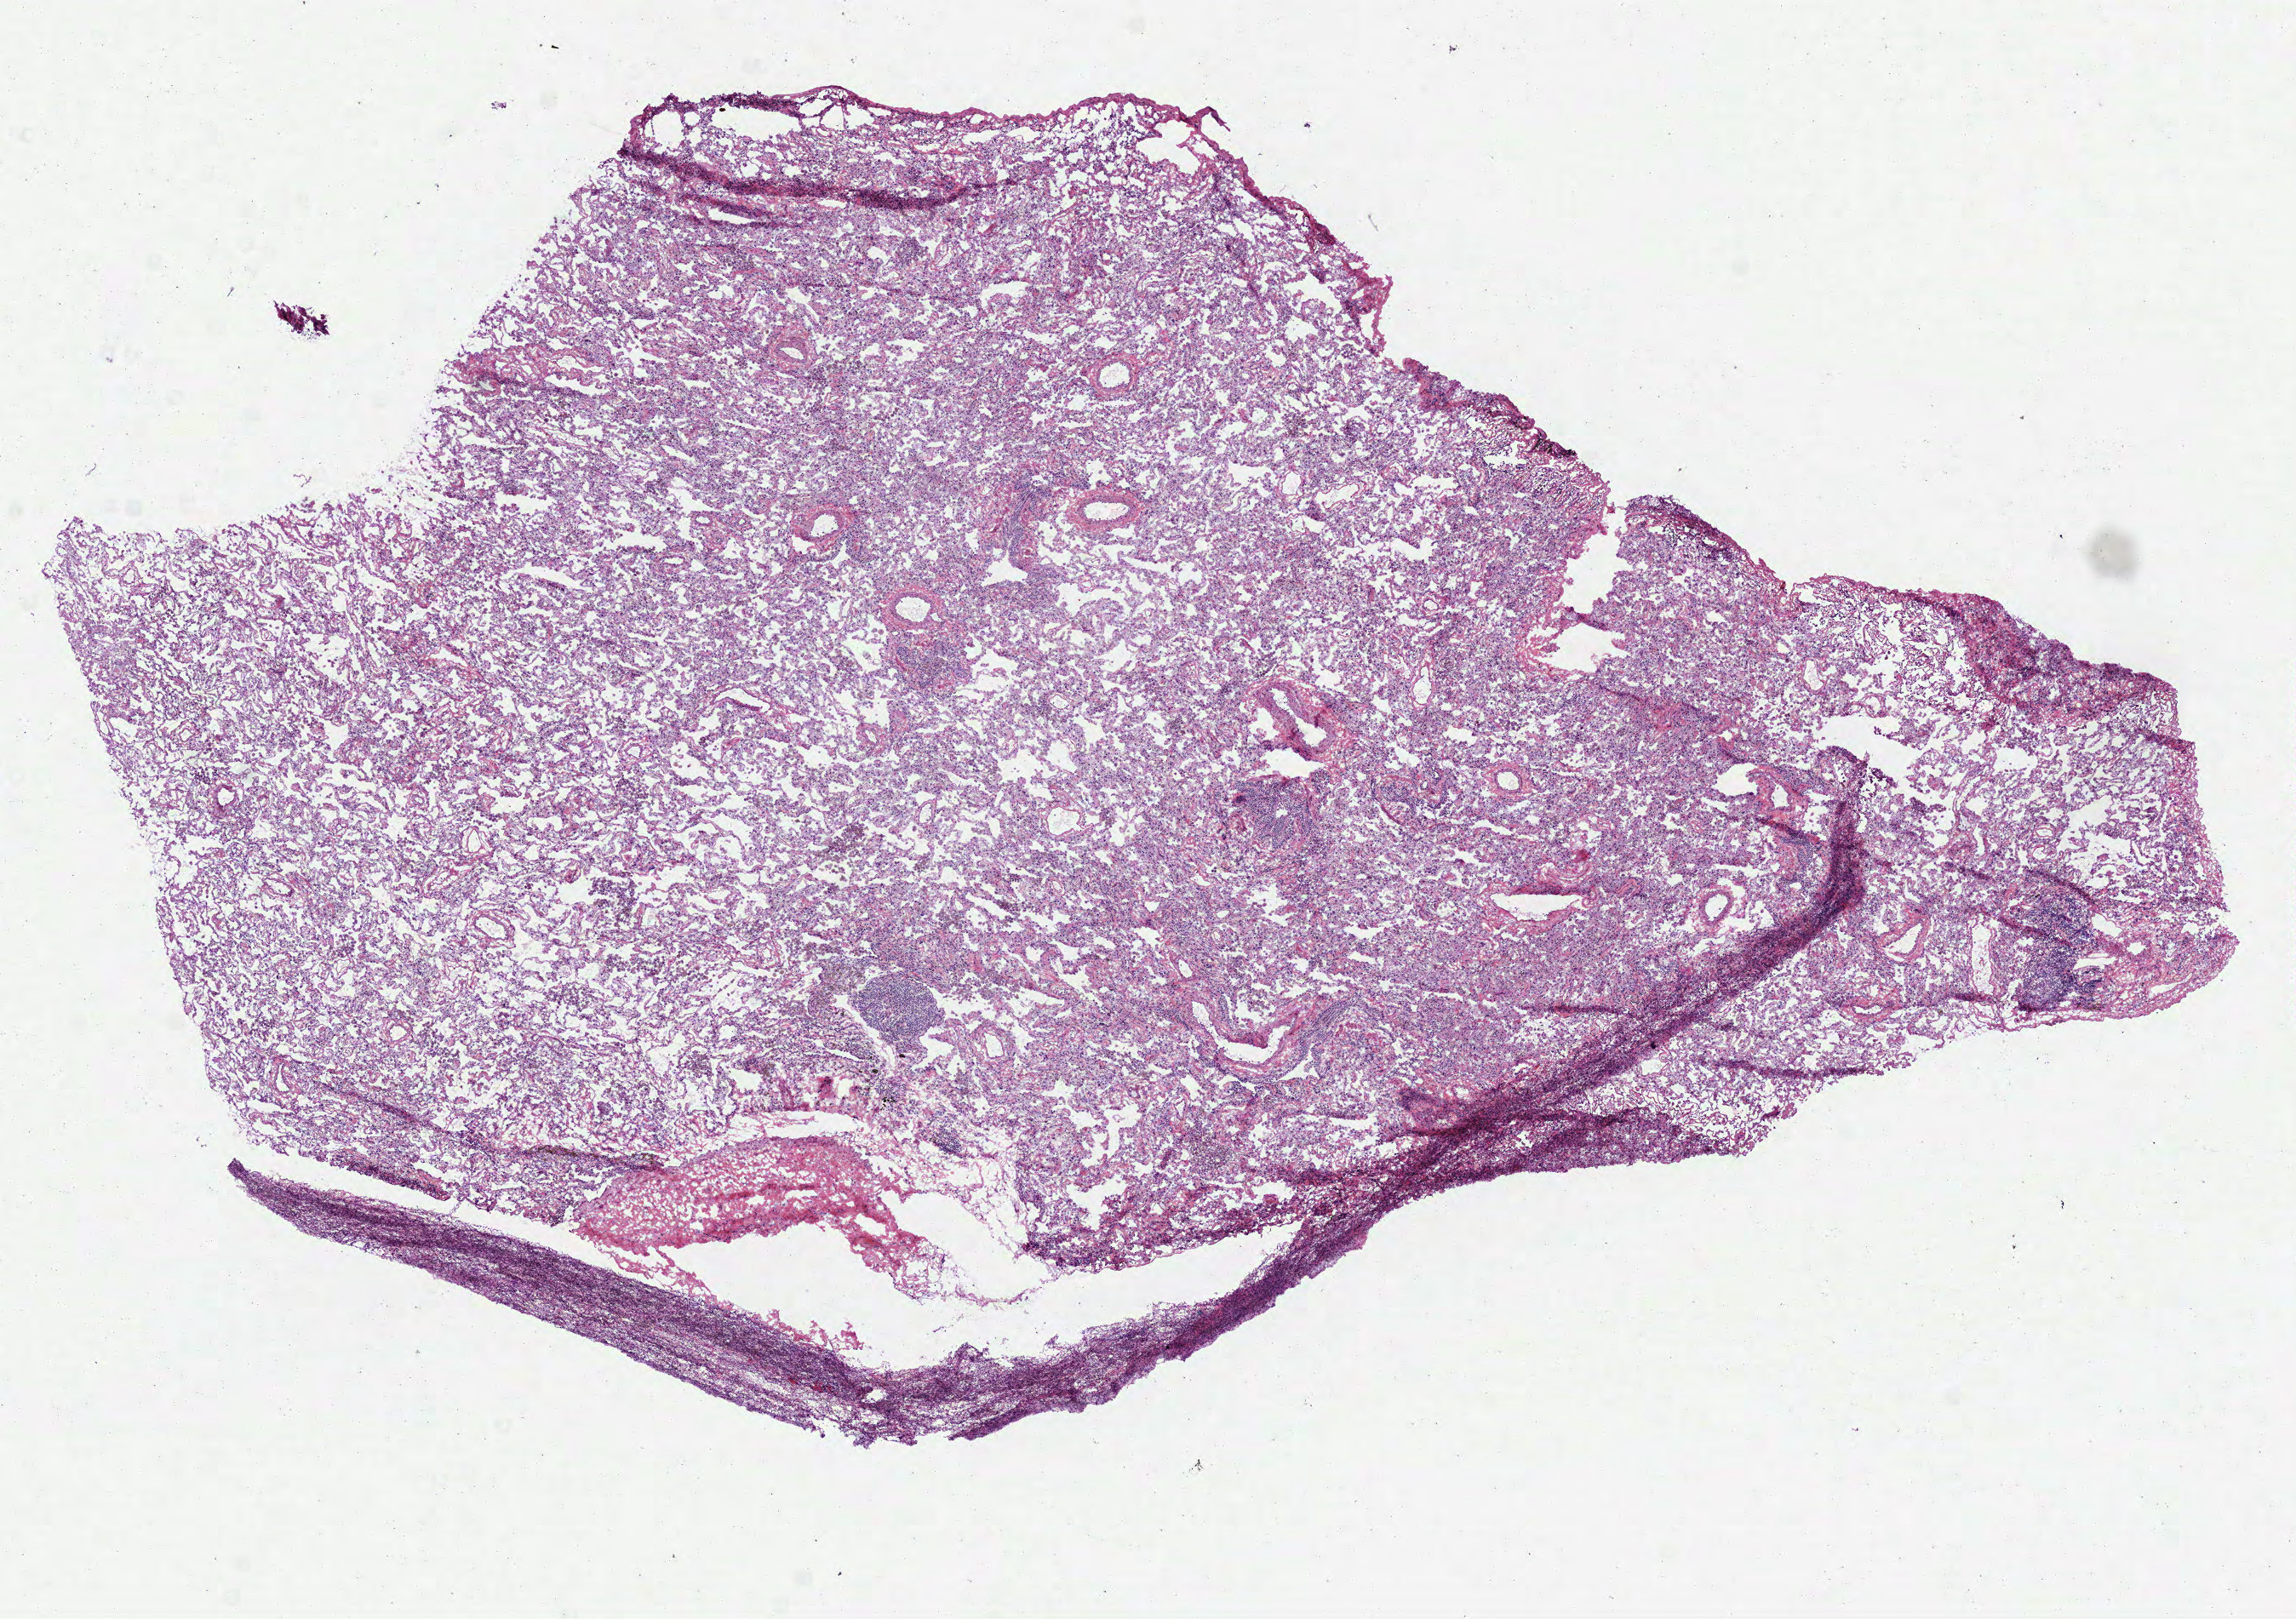
Hematoxylin and eosin (H&E) stained whole-slide image — low-resolution overview of the scanned area, about 10.9 x 7.7 mm (slide scanned at 40x), frozen section, lung, solid tissue normal (non-tumour tissue) sample. Patient: female, age at initial diagnosis 61 years.
This section: solid tissue normal (non-tumour) sample from the same patient. Patient diagnosis: Adenocarcinoma, NOS.